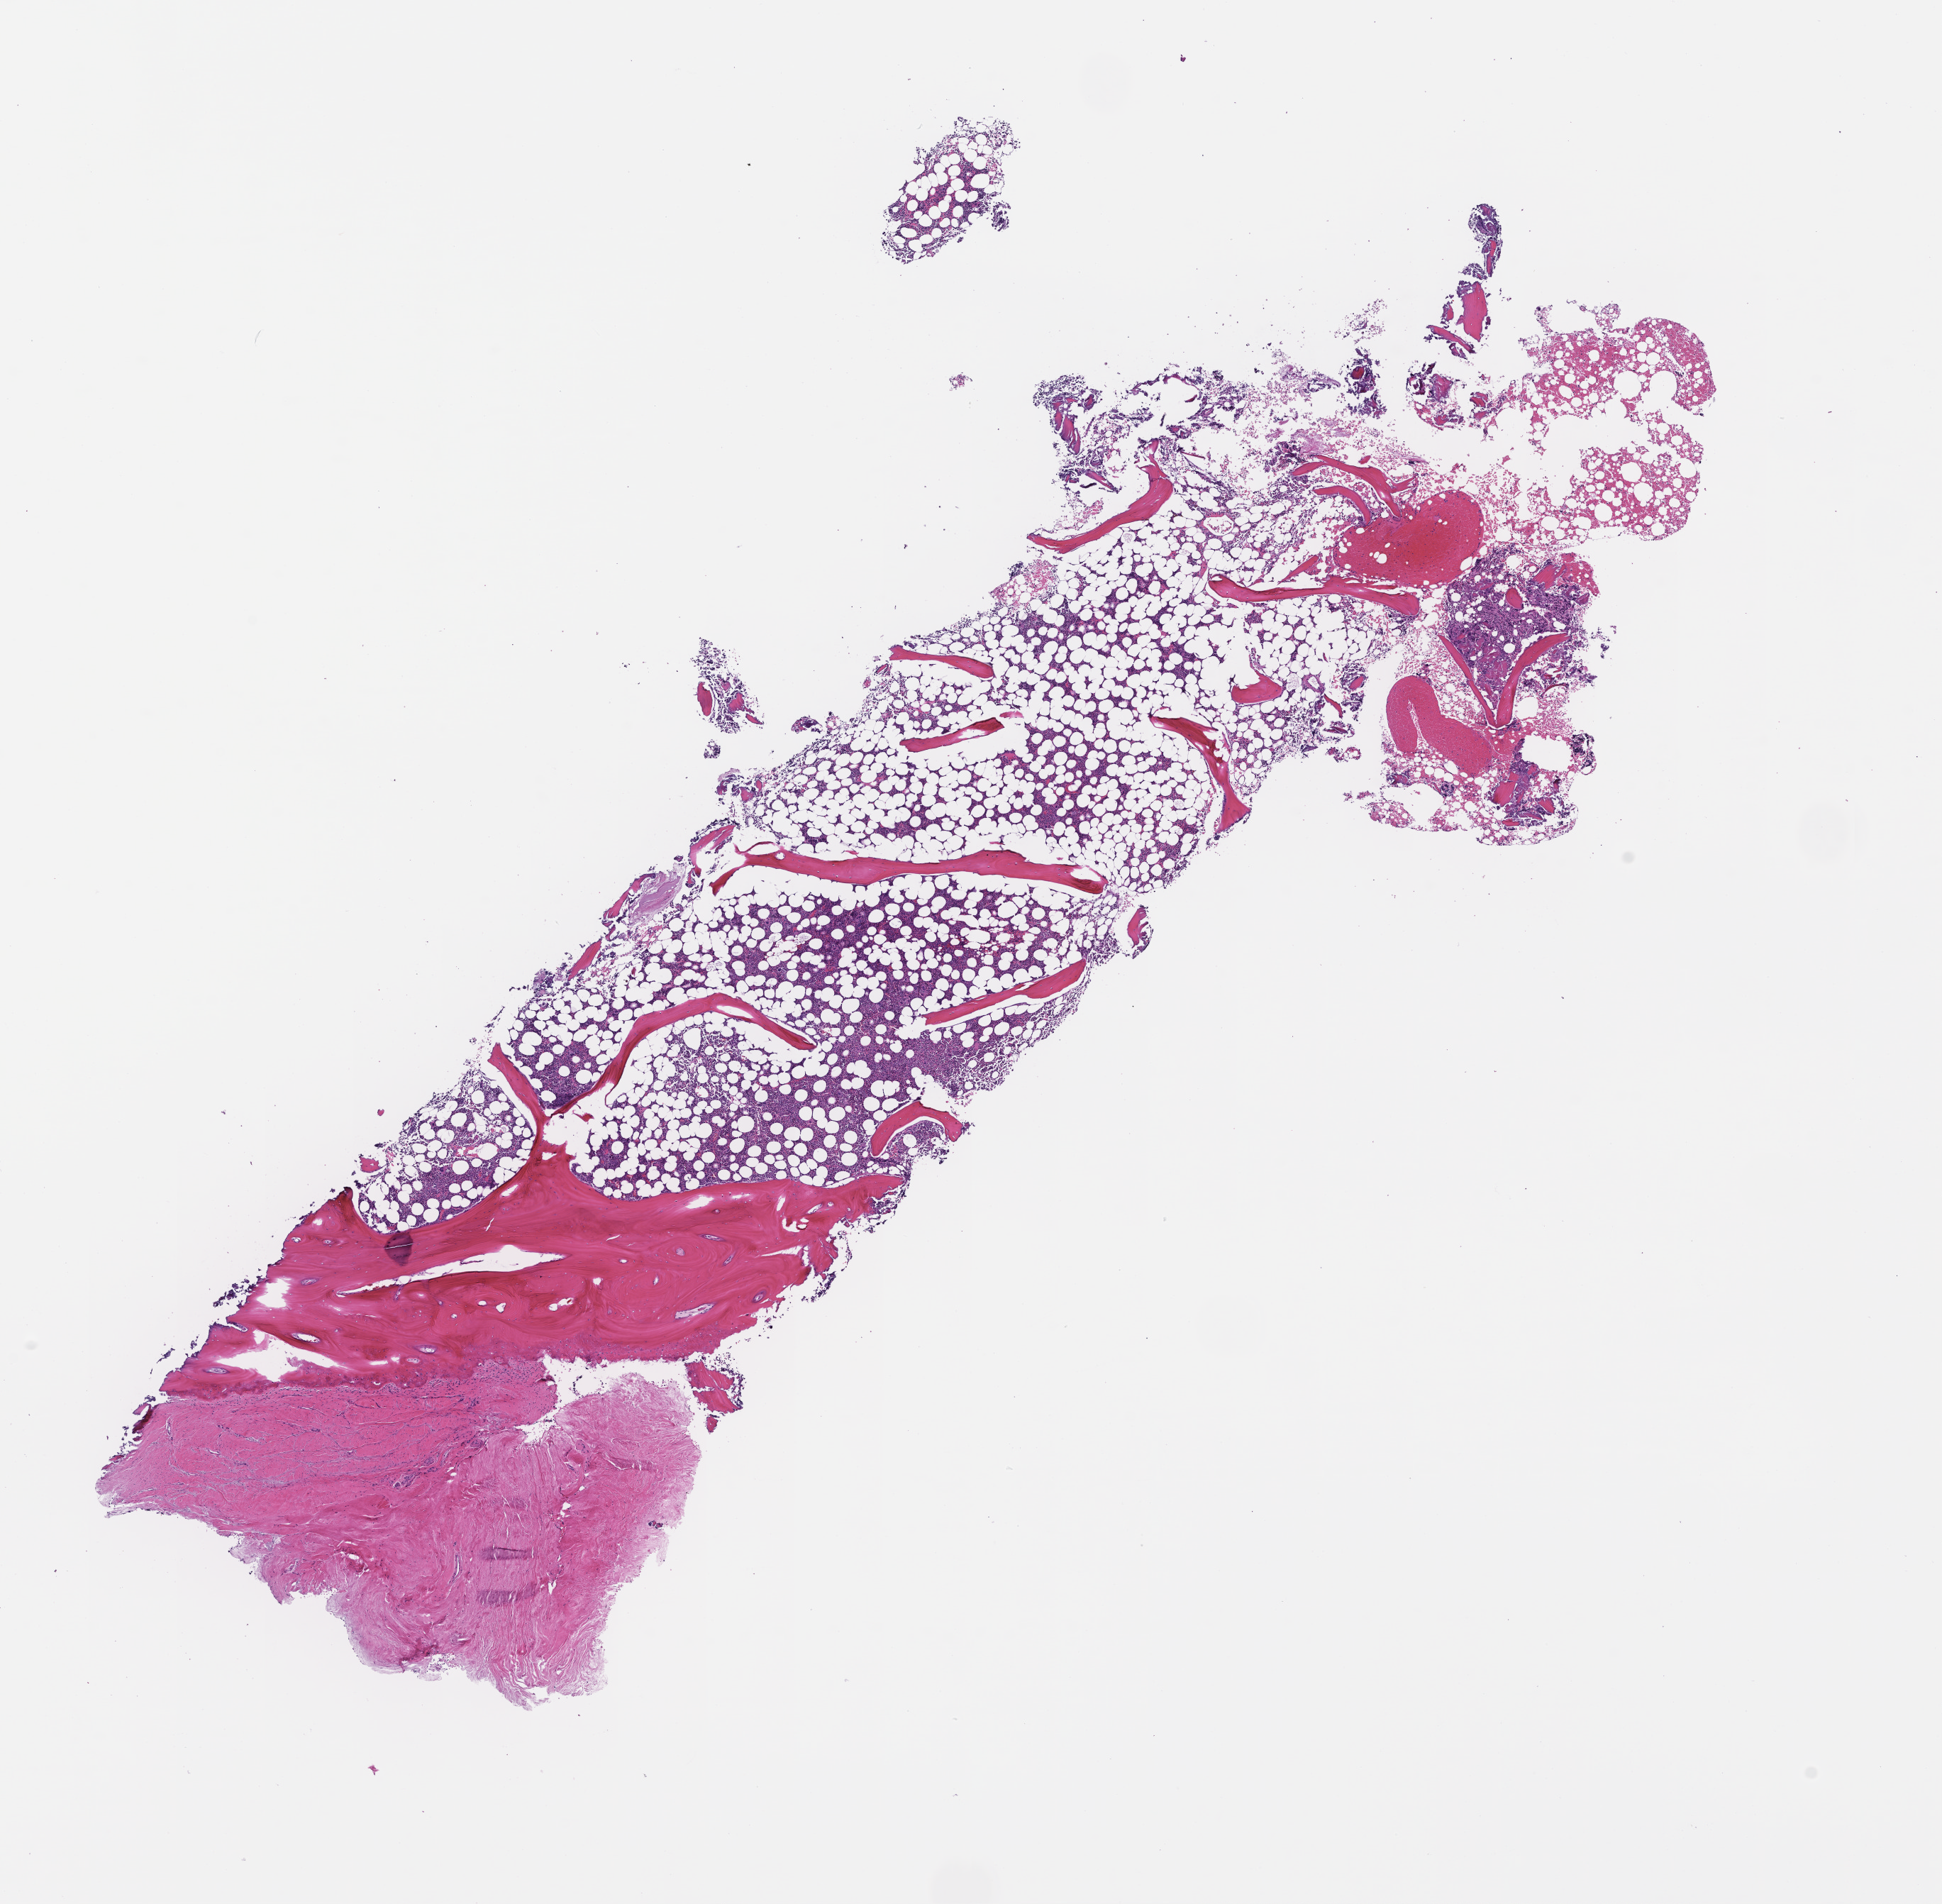
Hematoxylin and eosin (H&E) whole-slide image, a low-resolution overview of the entire scanned area, about 11.1 x 10.8 mm; formalin-fixed paraffin-embedded section; tissue site: bone marrow; collected at baseline (before treatment). Female patient.
• this section: primary tumour tissue
• diagnosis: Plasma Cell Myeloma